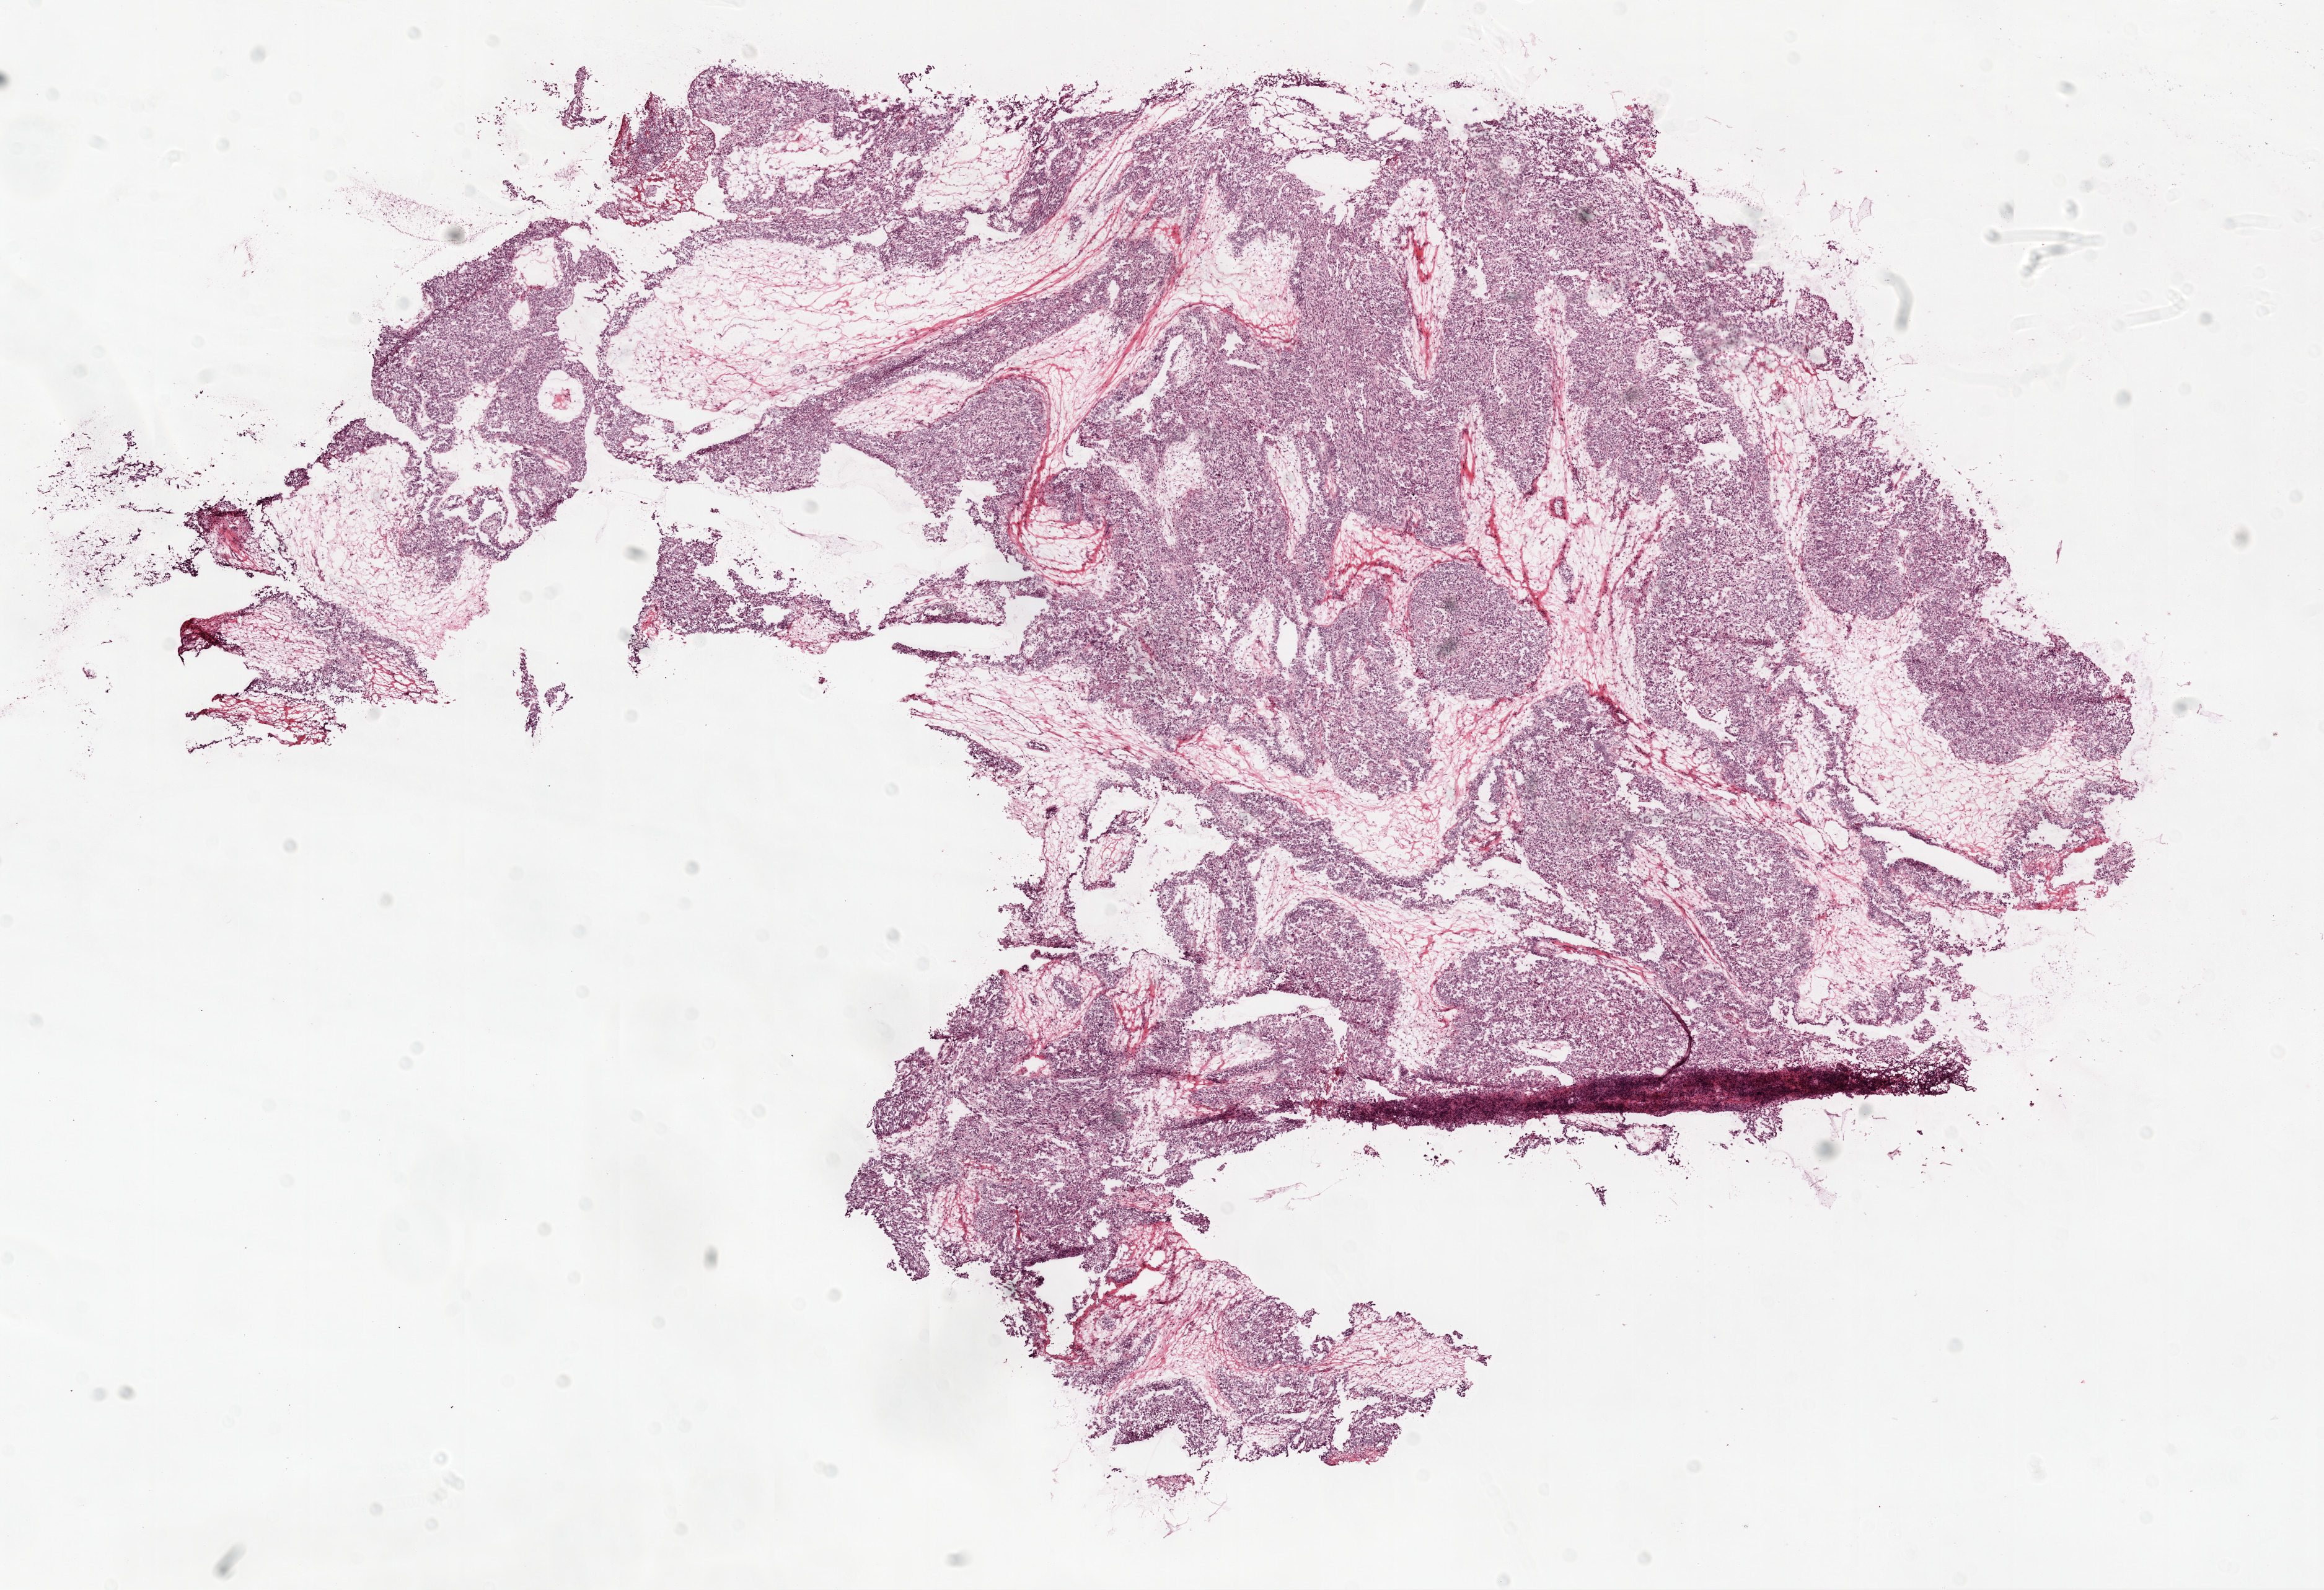
H&E-stained whole-slide image — whole scanned area (about 15.0 x 10.3 mm, acquisition: 20x scan) shown as a low-resolution overview, frozen section from the top of the tissue portion, ovary, primary tumour sample. Female, age 77 years at initial diagnosis. Histologic grade: G3 (poorly differentiated). Slide review estimates, as recorded: tumour cells 80%, tumour nuclei 80%, normal cells 0%, stromal cells 20%, necrosis 0%. Inflammatory infiltration, as recorded: lymphocyte infiltration 15%.
• pathologic diagnosis: Serous cystadenocarcinoma, NOS
• laterality: right
• FIGO stage: IIIC